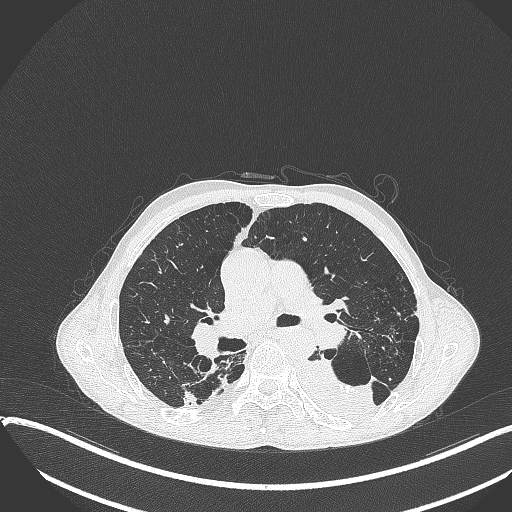
Chest CT, one axial slice. Position 229 of 401 along the scan axis. 120 kVp. Lung window (W 1500 / L -600 HU). 1 mm slice thickness. 512 × 512 image matrix. Patient: male, 57 years. Case-level facts recorded for this patient, not image findings: clinical TNM (as recorded): T4 N0 M0.
Outlined on this slice (rectangle marked by the reading radiologist):
- lung tumour (recorded histology: squamous cell carcinoma): box from (x=292, y=350) to (x=379, y=426) px